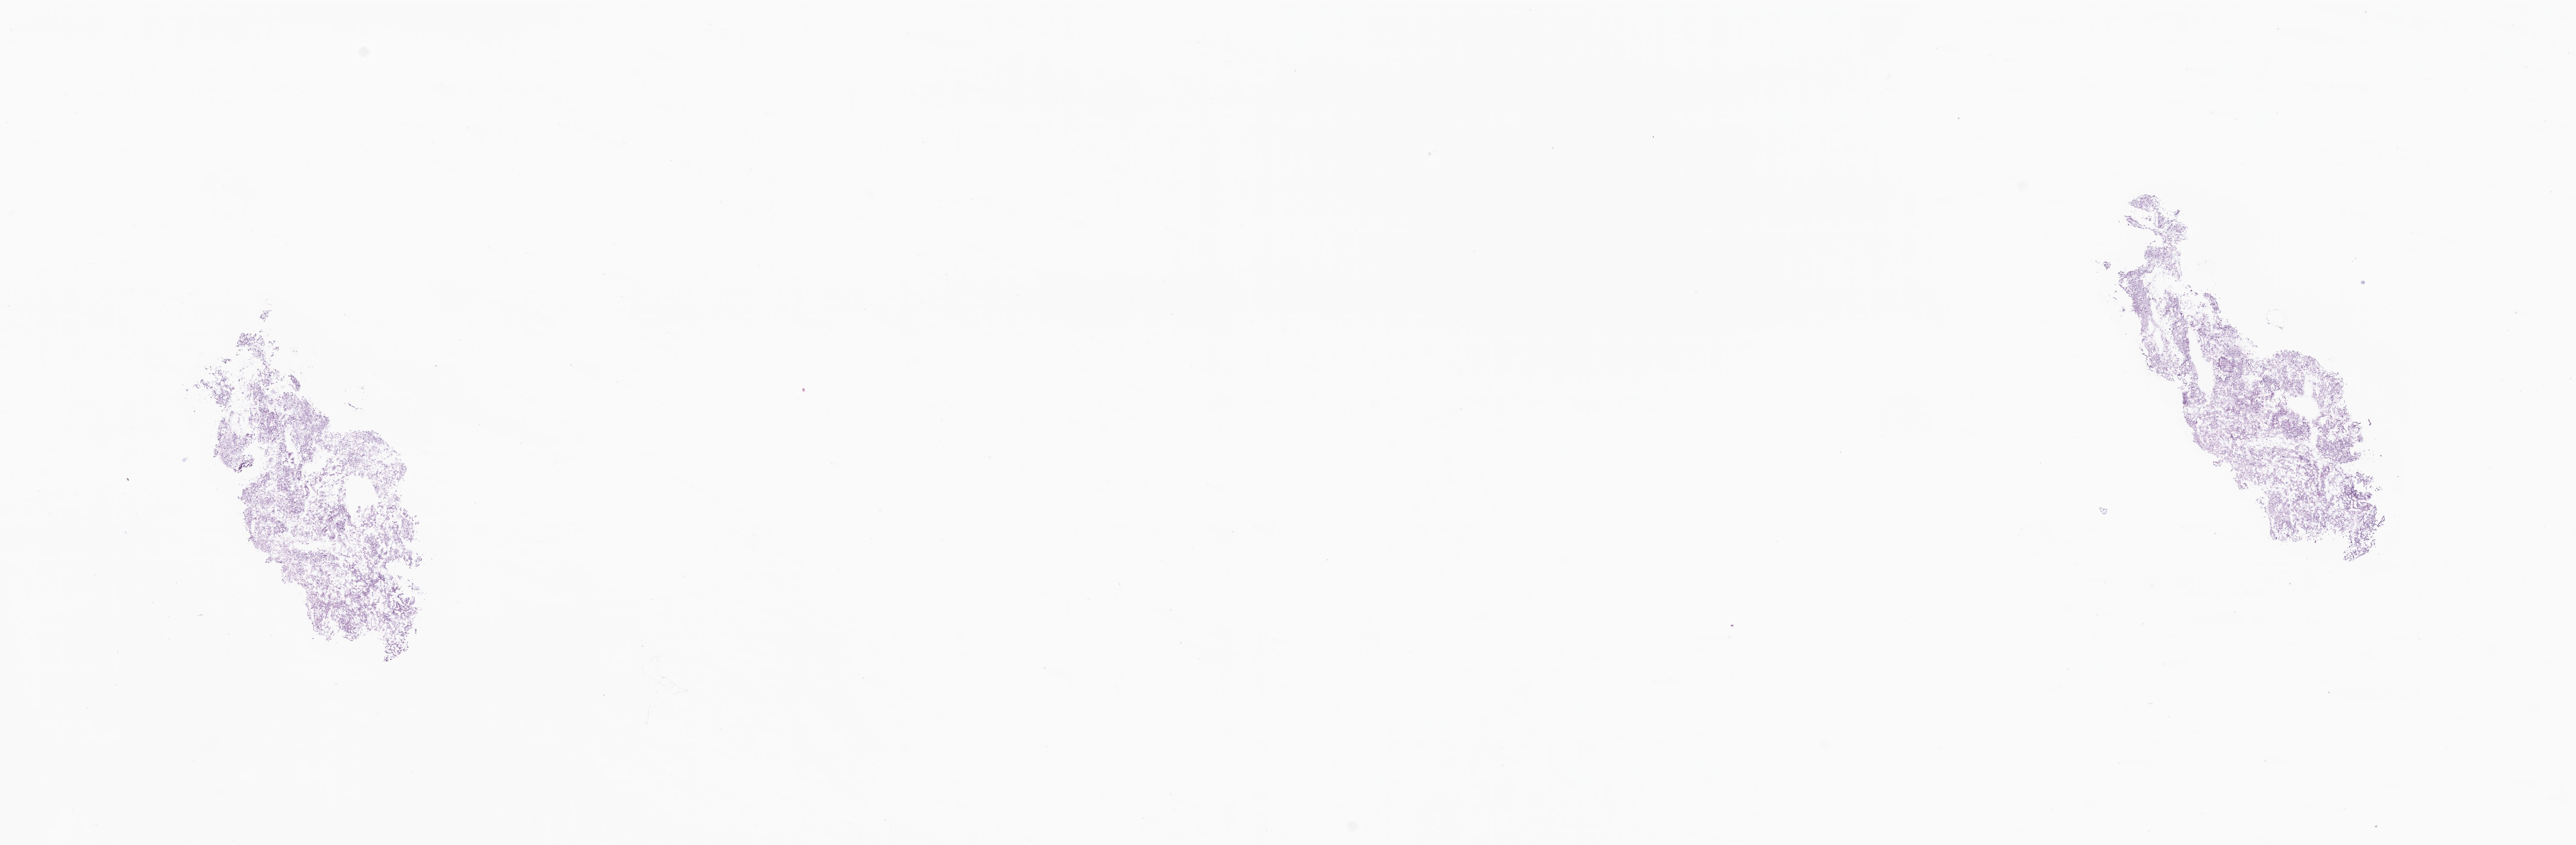
Digitized haematoxylin and eosin-stained section of tumor tissue from the brain, a low-resolution overview of the entire scanned area, about 25.1 x 8.2 mm; frozen section (OCT-embedded). Patient: male, age 138 months (11 years 6 months).
Recorded diagnosis: Pilocytic astrocytoma.